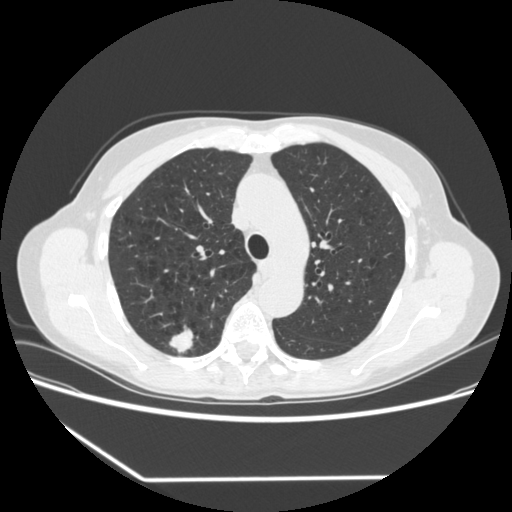
Axial slice from a low-dose chest CT screening exam; first (baseline) screen; lung window (W 1500 / L -600 HU); 1.25 mm slice thickness; slice 240 of 323 in the series; 512 × 512 image matrix. Female participant, aged 67 years at enrolment. Current smoker at enrolment.
Expert reader's lesion annotation, bounding box (x1, y1, x2, y2) in pixels: (157, 323, 201, 360). The screening reader recorded 2 non-calcified nodules or masses ≥4 mm on this exam (right upper lobe, right lower lobe); which of them this box marks is not recorded. Participant outcome: lung cancer diagnosed 29 days after this screen — adenocarcinoma, NOS, right upper lobe, moderately differentiated (G2), stage IA (AJCC 6th edition), 24 mm at pathology.